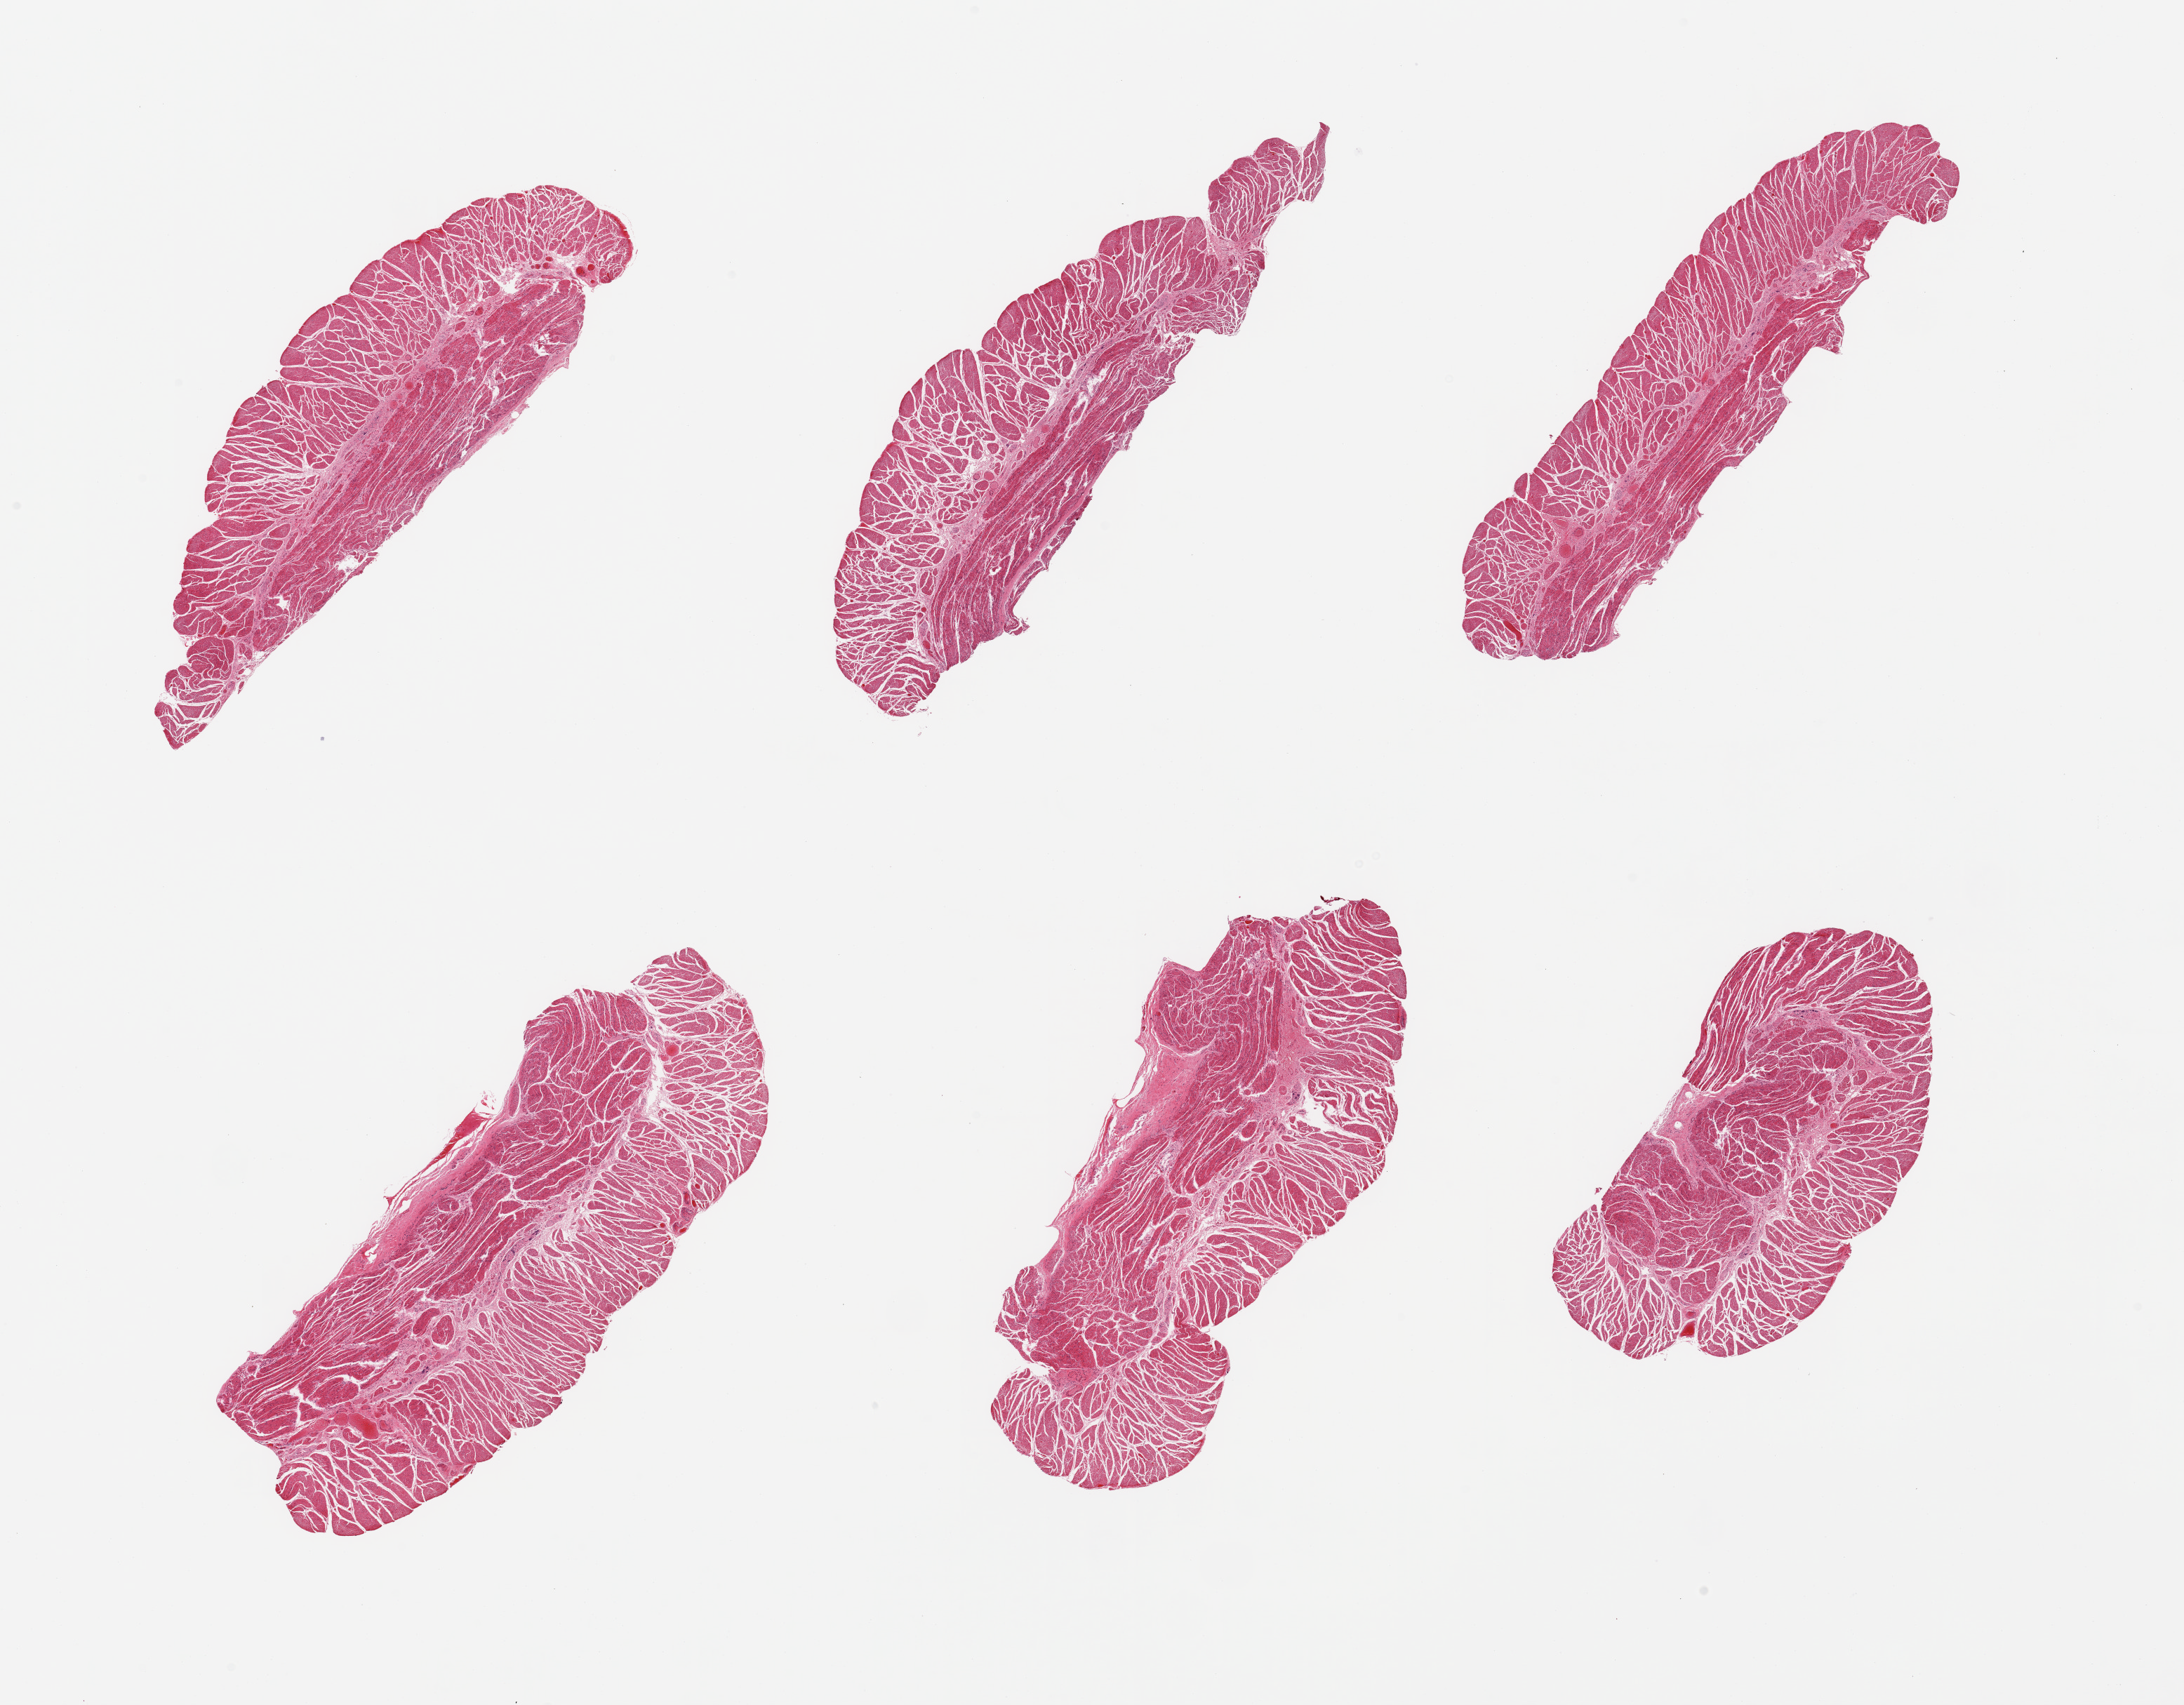
Whole-slide image, hematoxylin and eosin (H&E) stain, brightfield, shown as a low-resolution overview of the whole scanned area (about 24.6 x 19.2 mm, from a 20x scan); PAXgene-fixed, paraffin-embedded tissue; section of gastroesophageal junction (target tissue); donor tissue sample. Donor: male.
Reviewer comment on this tissue sample: 6 pieces; well trimmed.